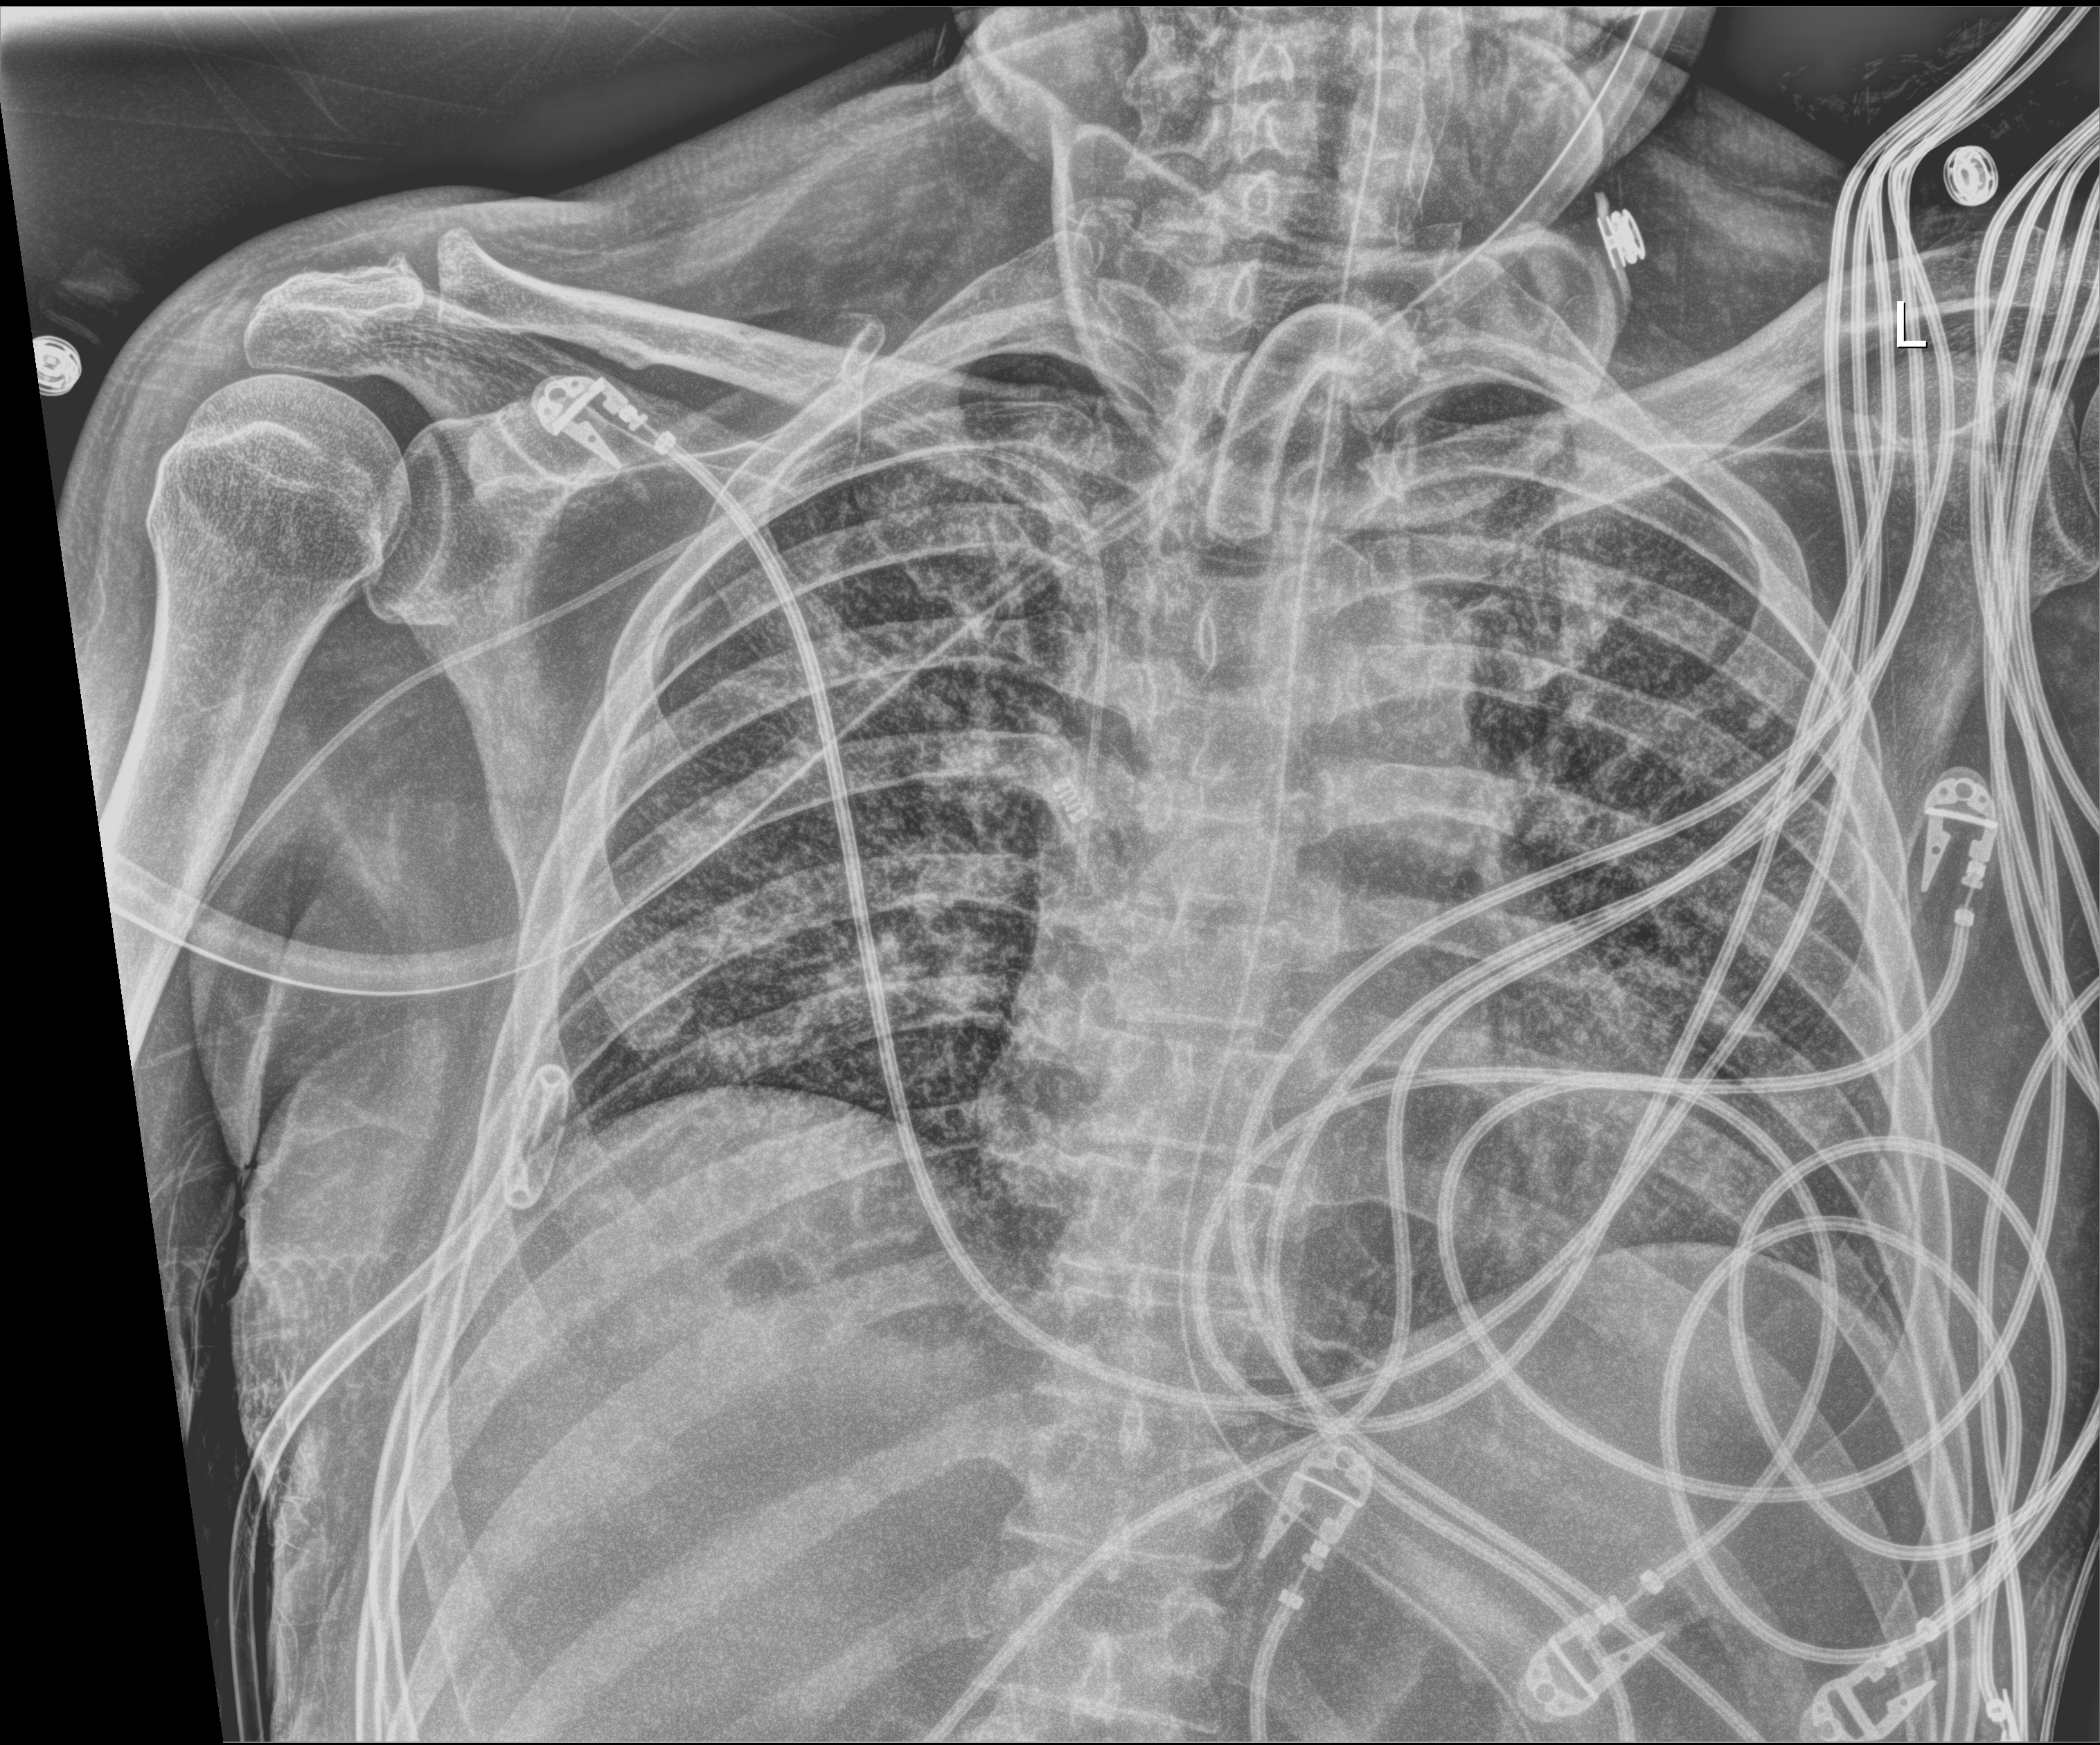
Portable chest radiograph, anteroposterior (AP) projection. Male patient hospitalised with COVID-19, age 18–59 years.
Admission-level facts for this patient (not findings on this image; timing relative to this image not recorded):
- length of hospital stay: 77 days
- diabetes (admission record): no
- mechanically ventilated during this hospital stay: yes